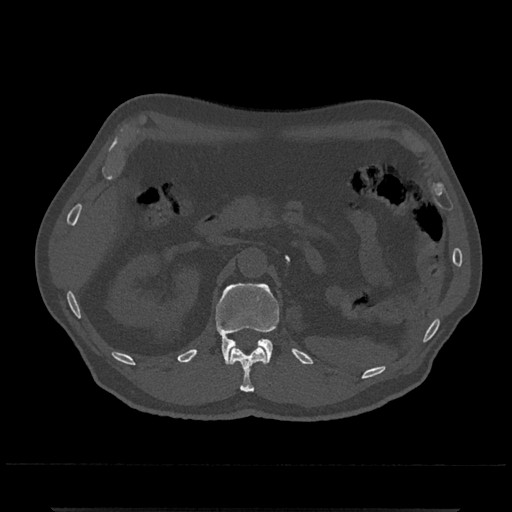
CT including the spine, one axial slice; position 389 of 797 along the scan axis; reconstruction kernel Br40s/3; 120 kVp; bone window (W 1800 / L 400 HU); 0.5 mm slice thickness; 512 × 512 image matrix, field of view 393 × 393 mm. Patient: male, 67 years. Case-level facts recorded for this patient, not image findings: primary cancer: prostate.
Outlined on this slice (semi-automatically segmented with operator editing):
- L1 vertebra: bounding box (x1, y1, x2, y2) in pixels: (215, 283, 280, 365)
- T12 vertebra: (230, 346, 267, 392)